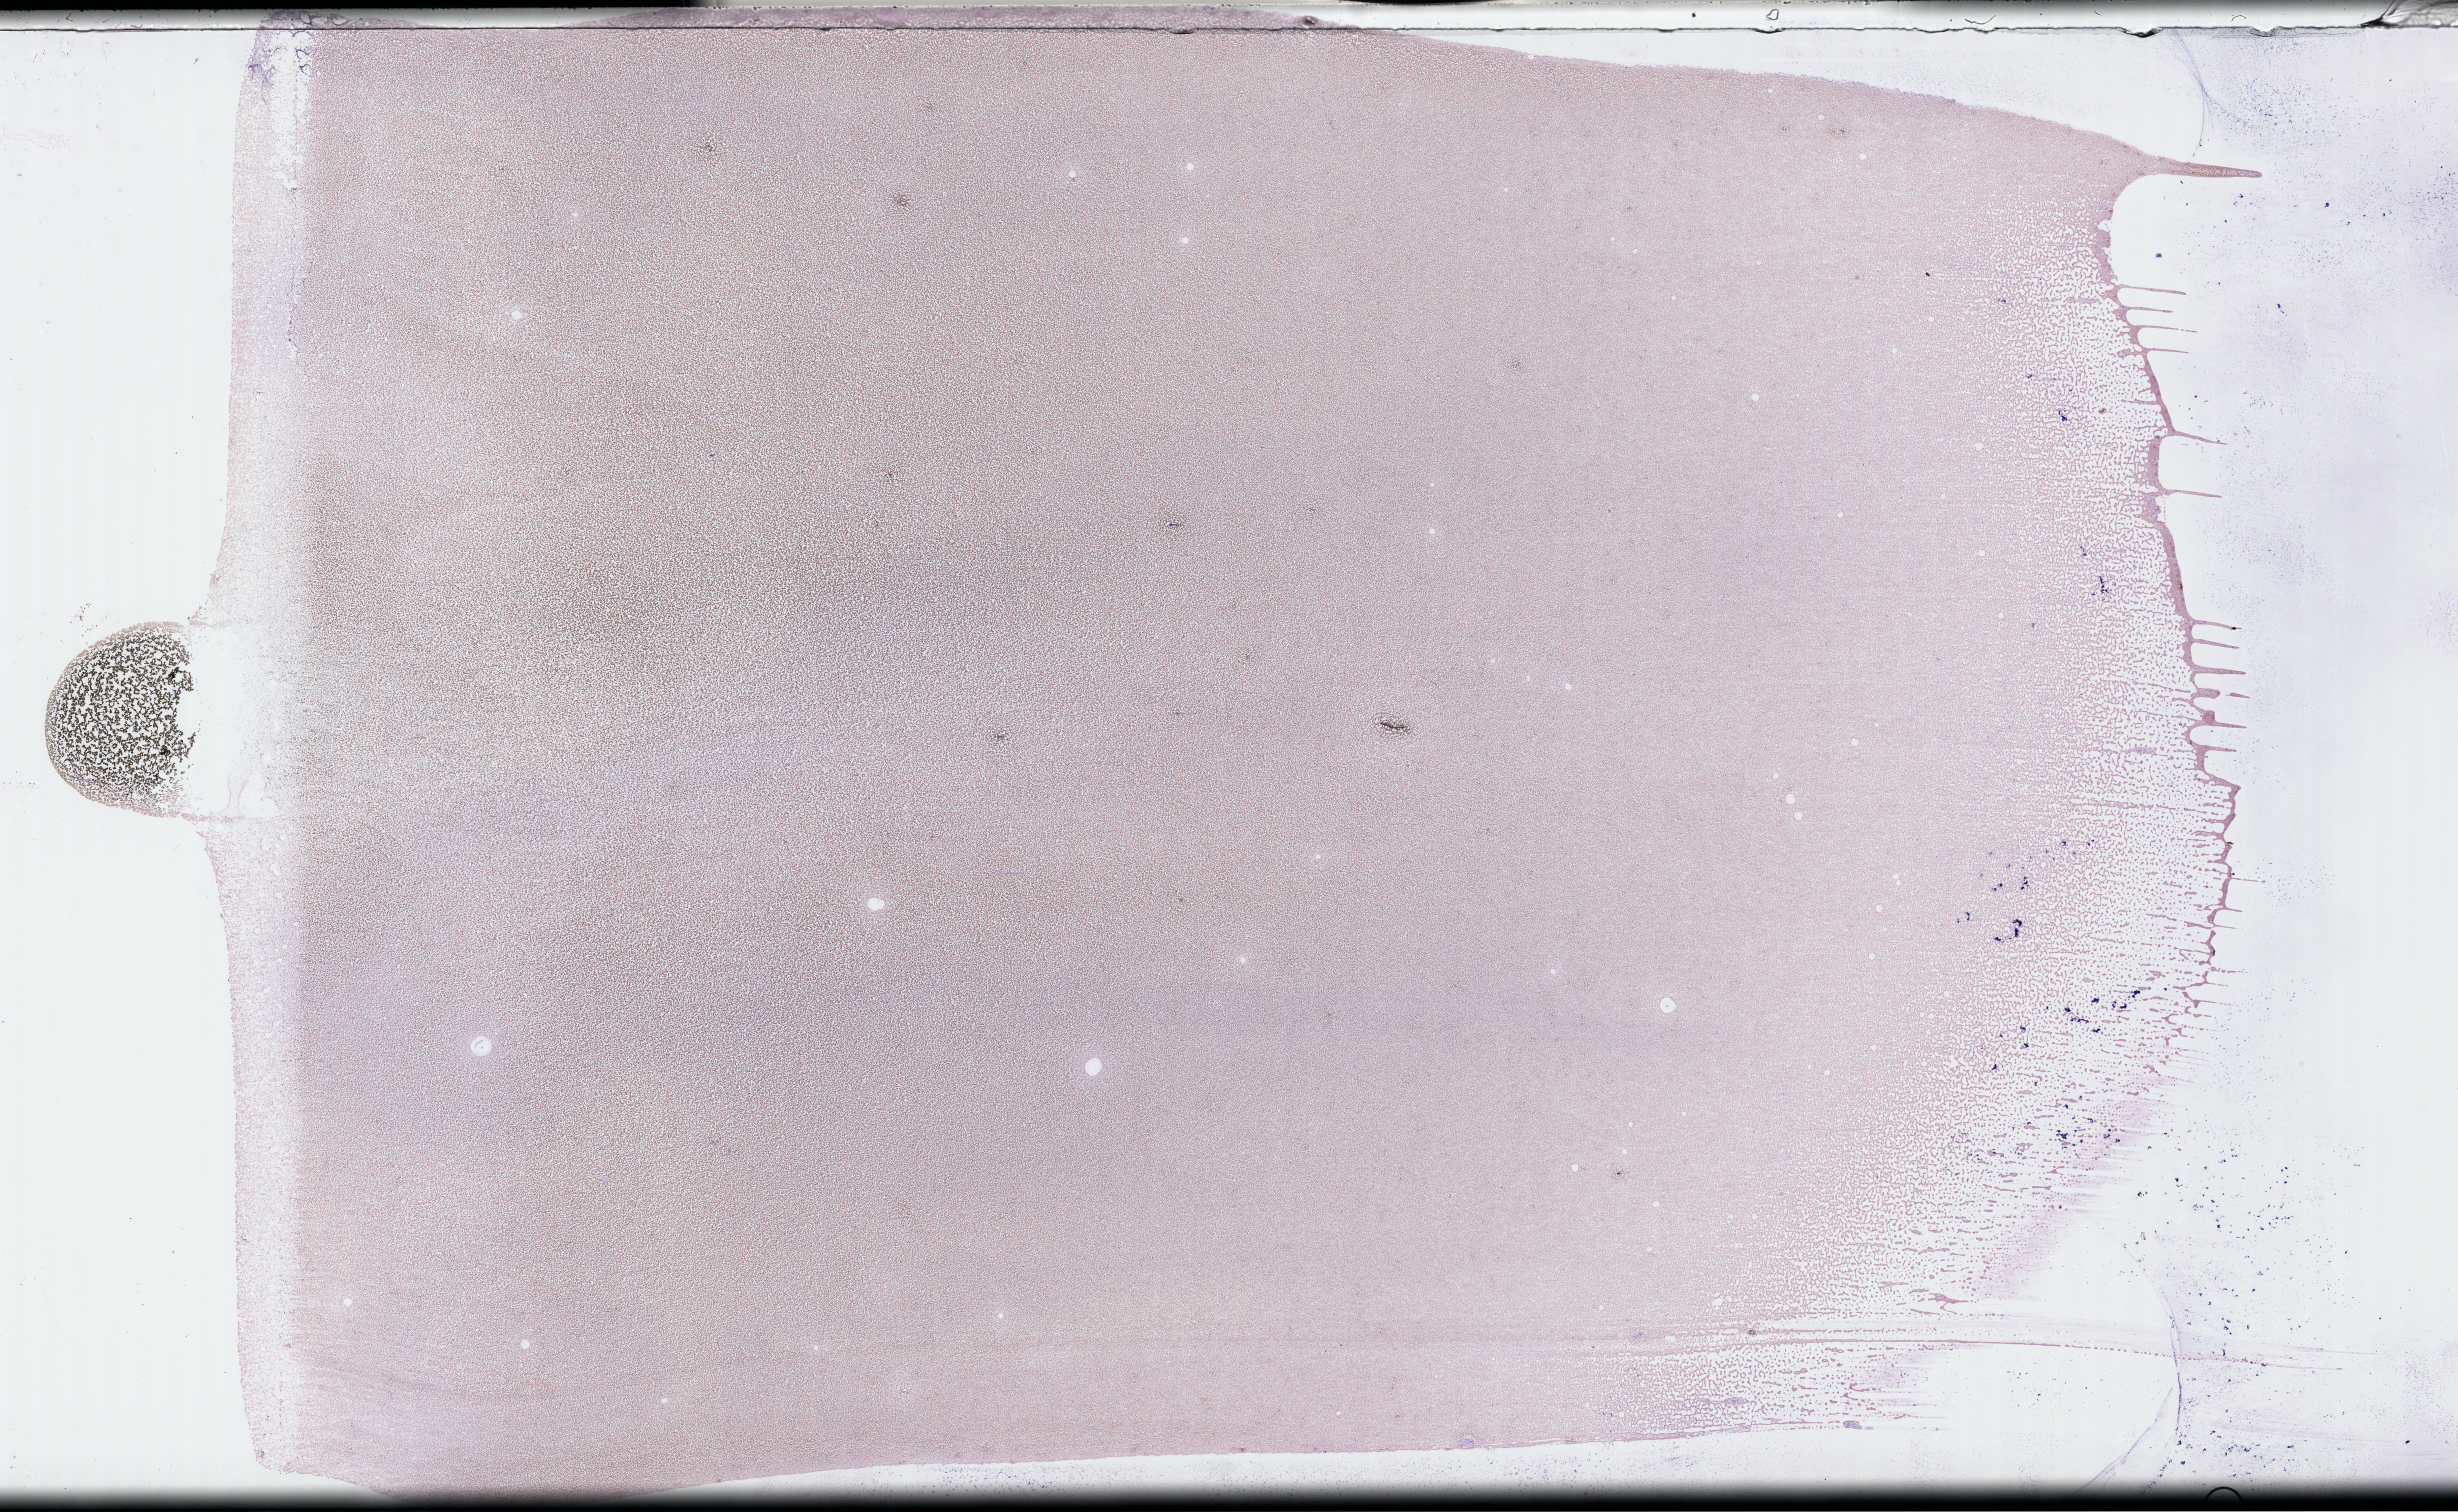
Whole-slide image of a whole blood smear, Wright–Giemsa stain — a low-resolution overview of the entire scanned area, about 39.7 x 24.4 mm. Specimen time point: collected at baseline (before treatment). Male patient.
Patient diagnosis: Plasma Cell Myeloma.